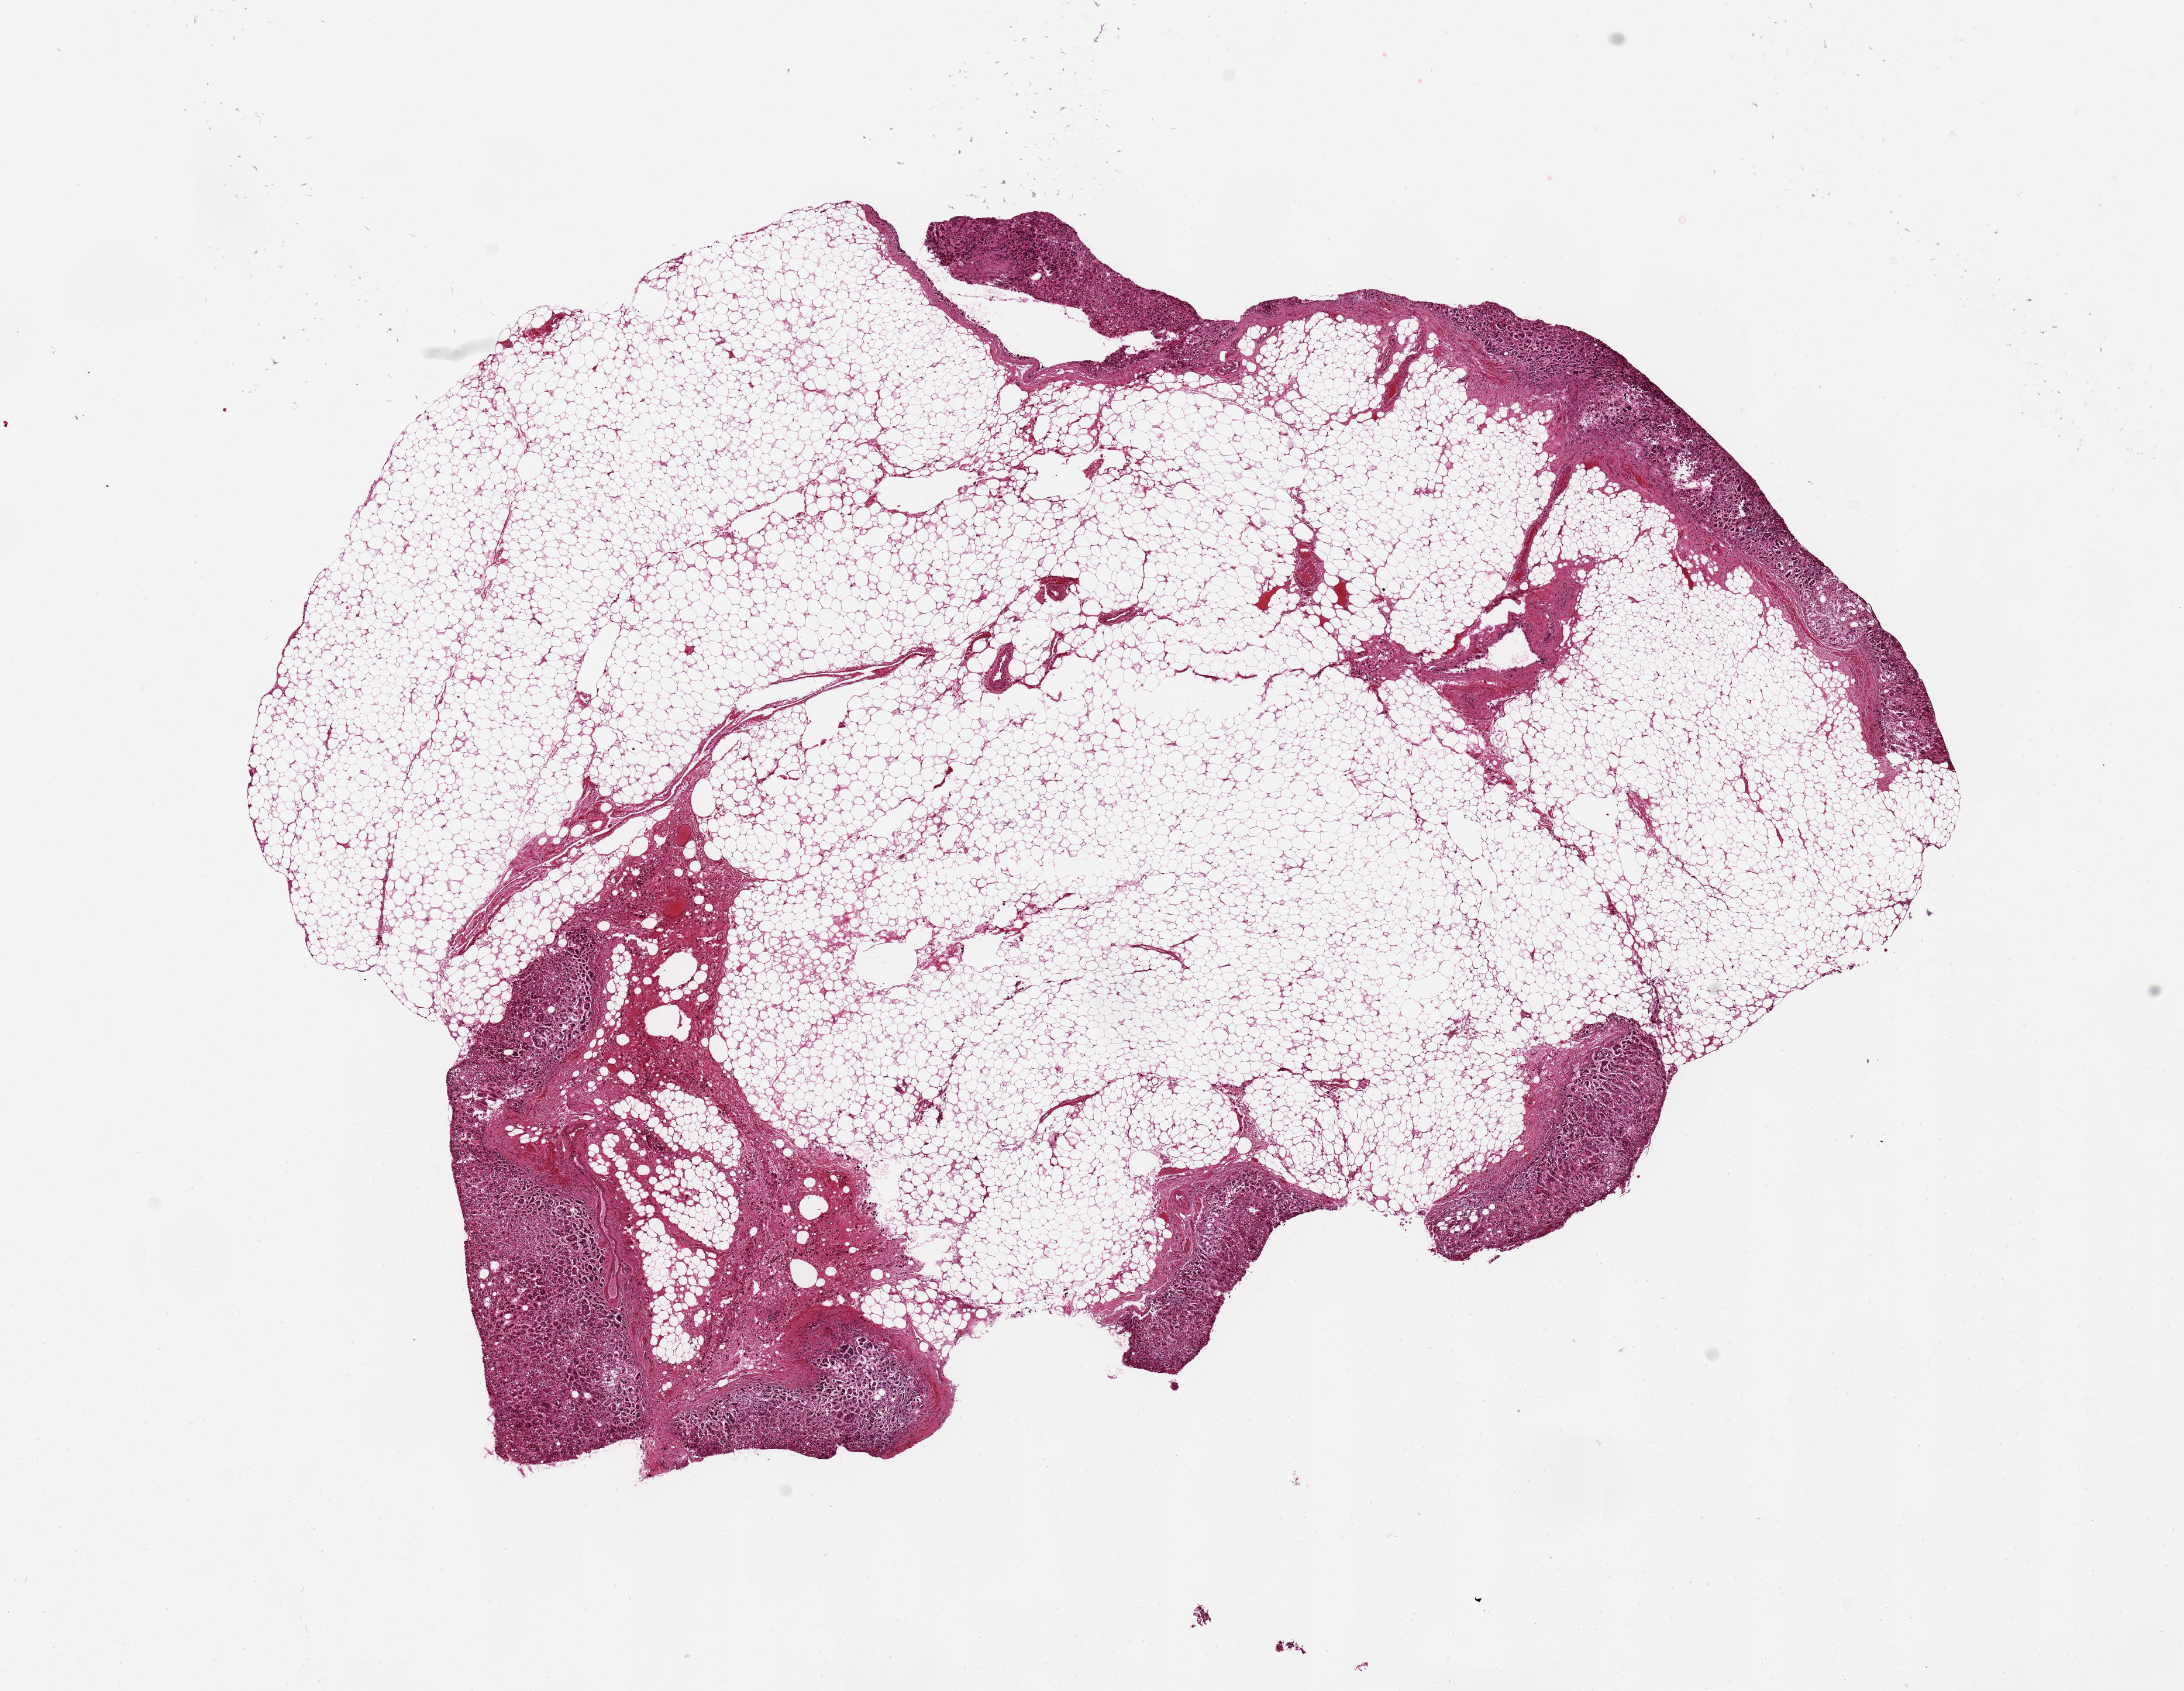
Whole-slide image, H&E stain, brightfield, a low-resolution overview of the entire scanned area, about 14.8 x 11.4 mm; PAXgene-fixed, paraffin-embedded tissue; target tissue: adrenal gland; tissue donor sample. Female donor.
- review note (as recorded): 11x8mm. Central 80% is fat, 2.2x3.8mm nodule of cortex on one edge; thin 0.5mm rim of cortex on opposite edge